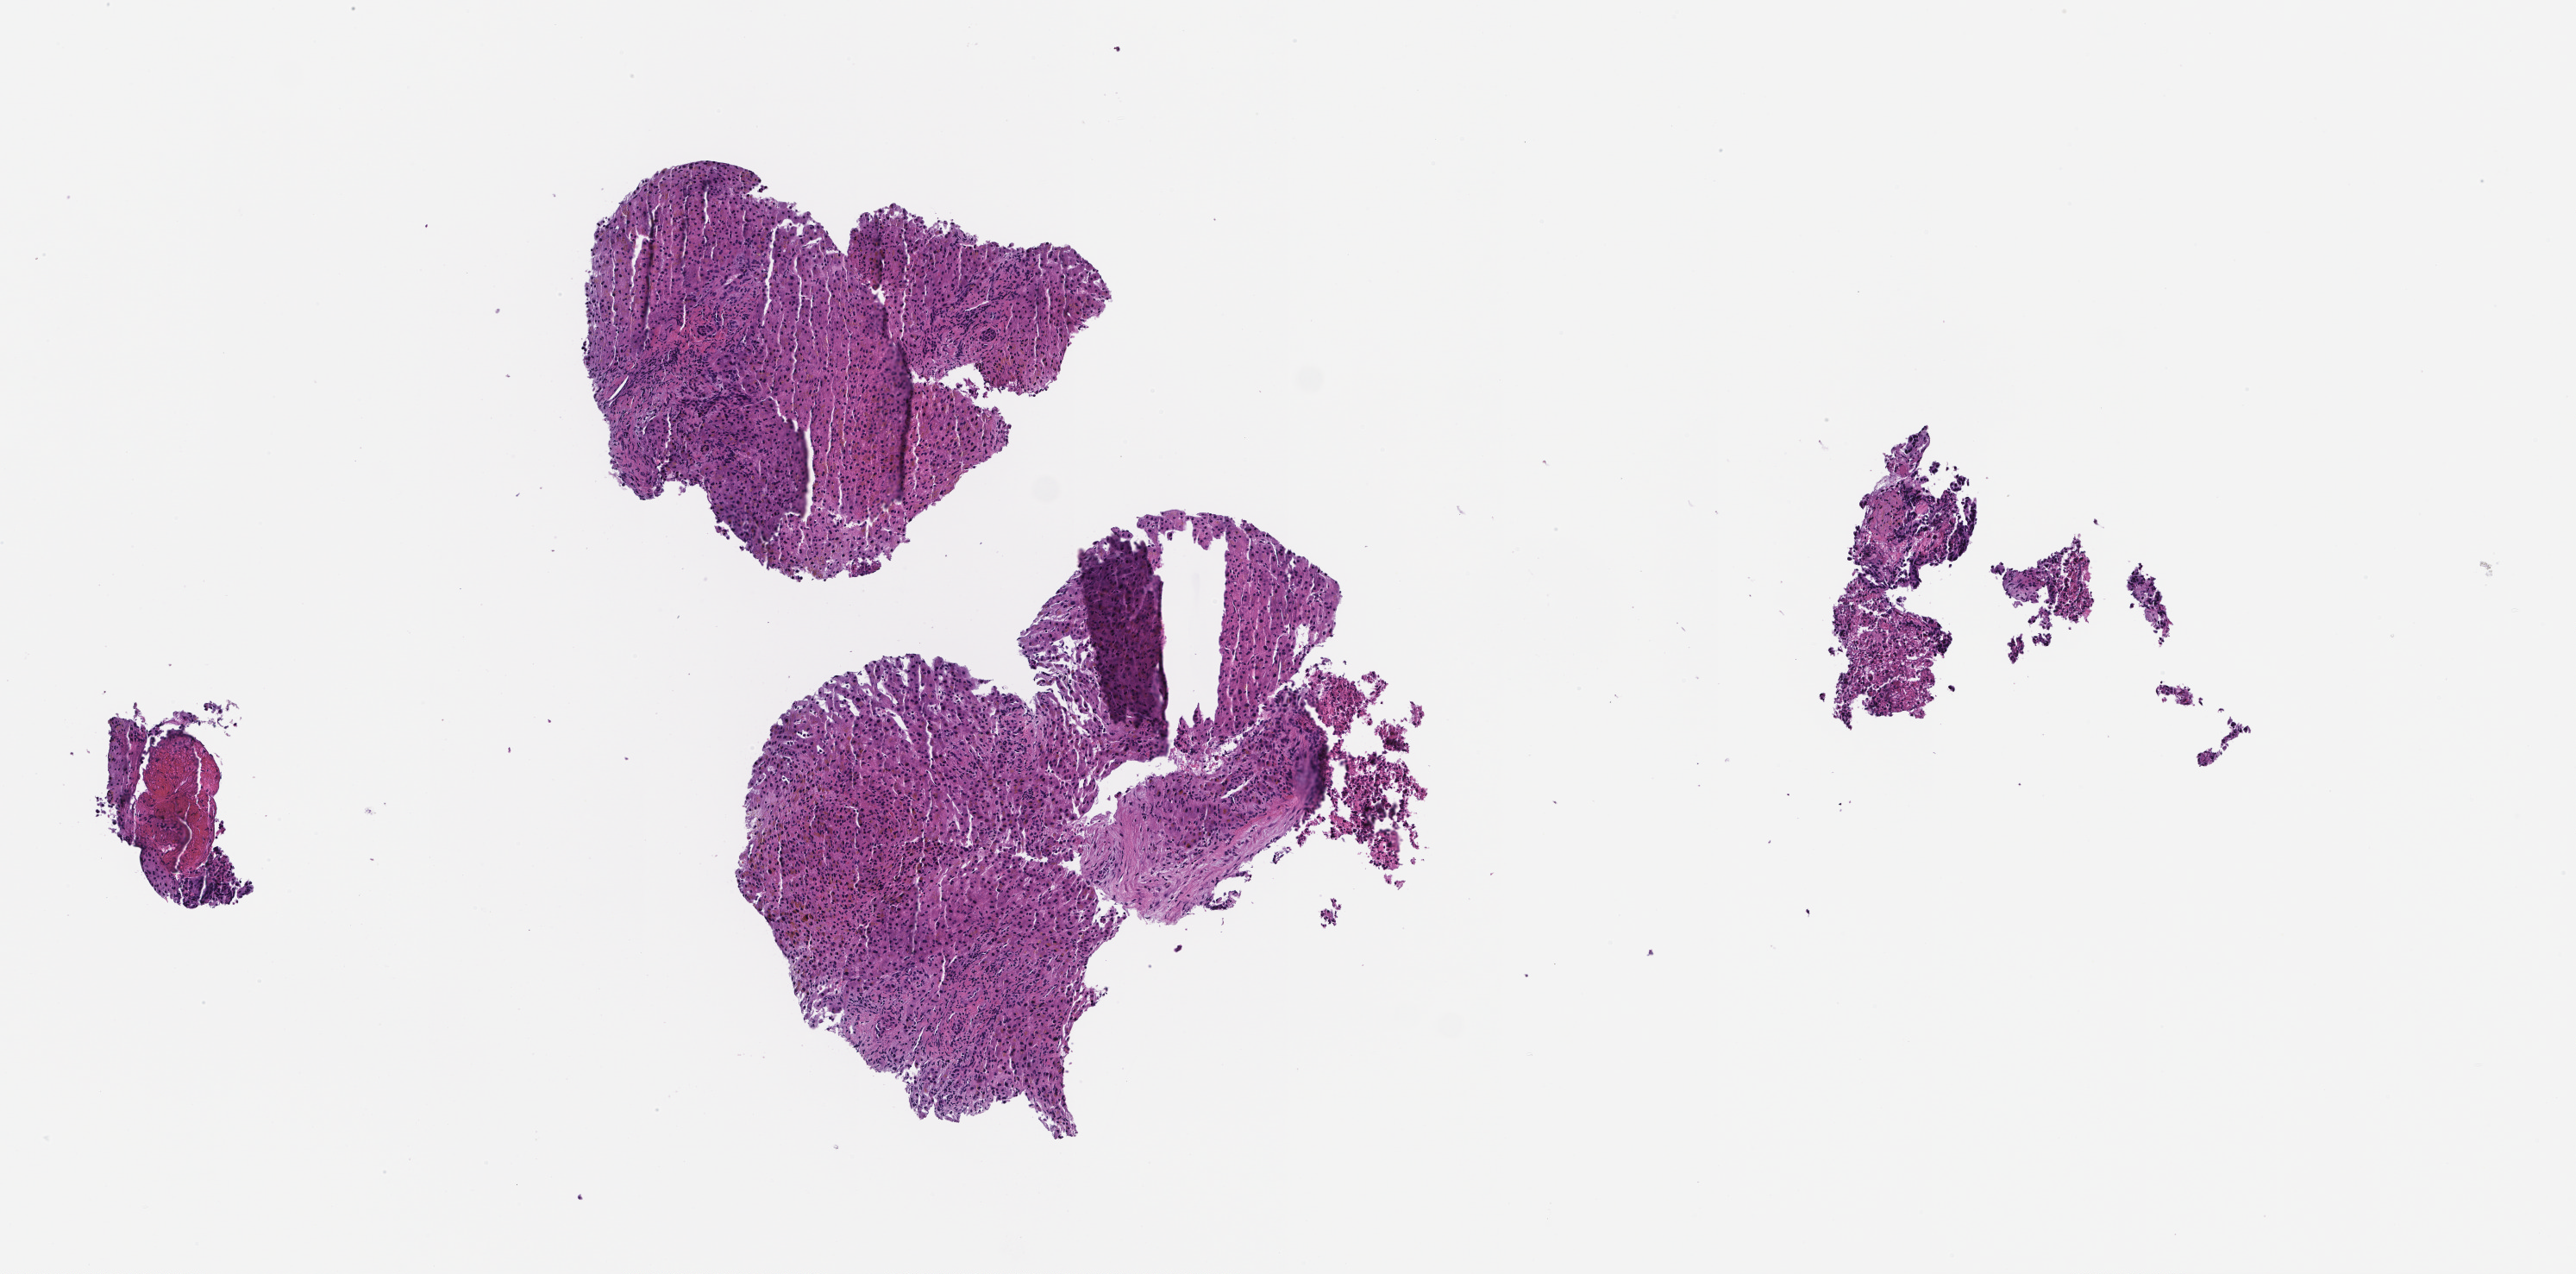
Digitized H&E-stained section — whole scanned area (about 6.0 x 3.0 mm) shown as a low-resolution overview. Formalin-fixed, paraffin-embedded (FFPE) tissue. Collected at baseline (before treatment). Patient: female.
* this section: metastatic tumor tissue
* patient diagnosis (primary): Colorectal Carcinoma